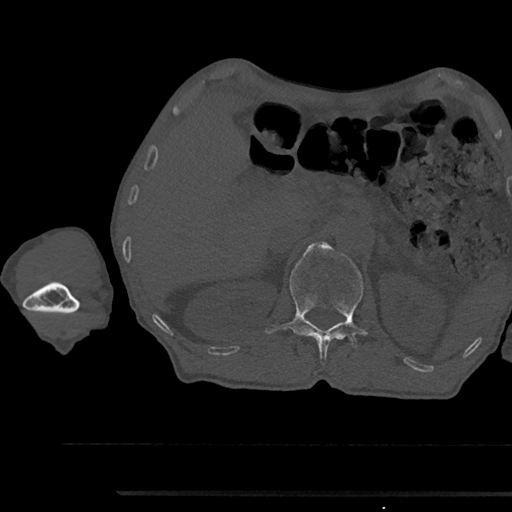
CT including the spine, one axial slice; reconstruction kernel Br40s/3; 120 kVp; bone window (W 1800 / L 400 HU); 0.5 mm slice thickness; 512 × 512 image matrix. Male patient, age 79 years. Case-level facts recorded for this patient, not image findings: primary cancer: prostate.
Annotated regions visible in this slice (semi-automatic segmentation, software-assisted and operator-edited):
- L1 vertebra: bounding box <265,241,367,361> (left, top, right, bottom; pixels)